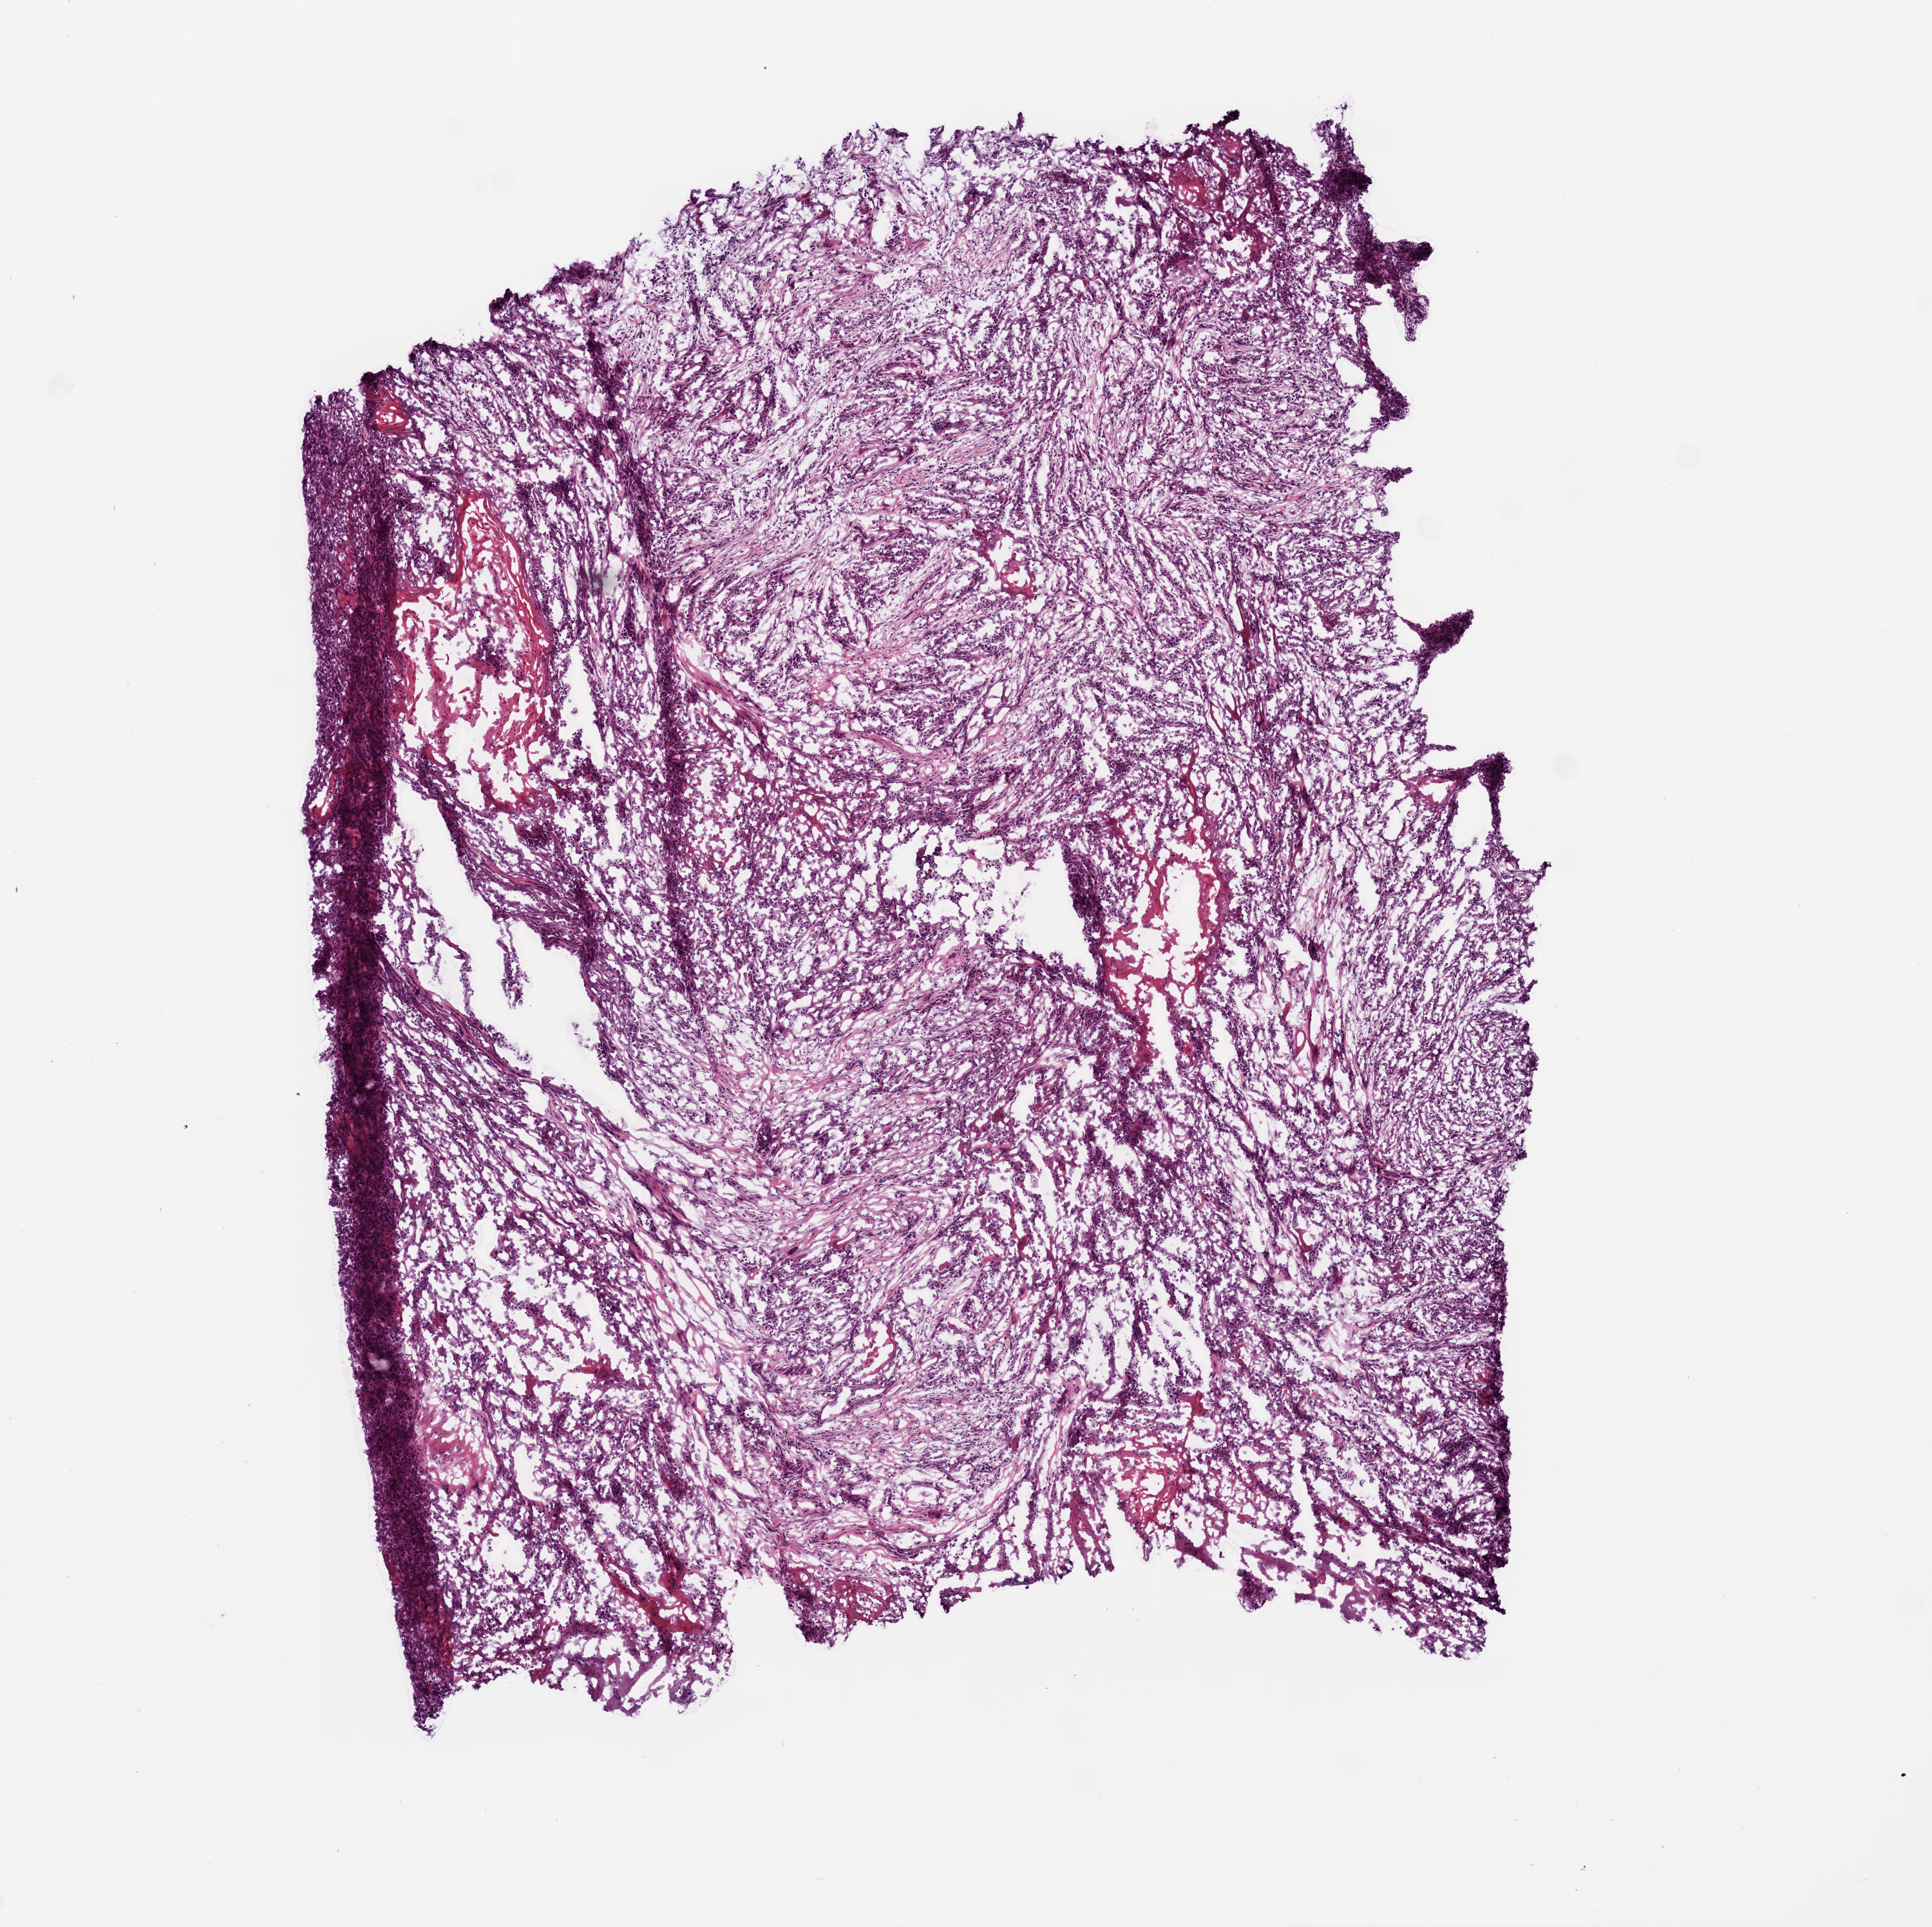
Digitized Hematoxylin and eosin (H&E) stained tissue section (whole slide) — a low-resolution overview of the entire scanned area, about 6.0 x 6.0 mm; frozen section; sample: primary tumour, head and neck. Male, age 74 years at initial diagnosis. Composition of this section per pathologist review: tumour cells 100%, tumour nuclei 70%.
Histologic diagnosis: Squamous cell carcinoma, NOS (tongue, NOS).